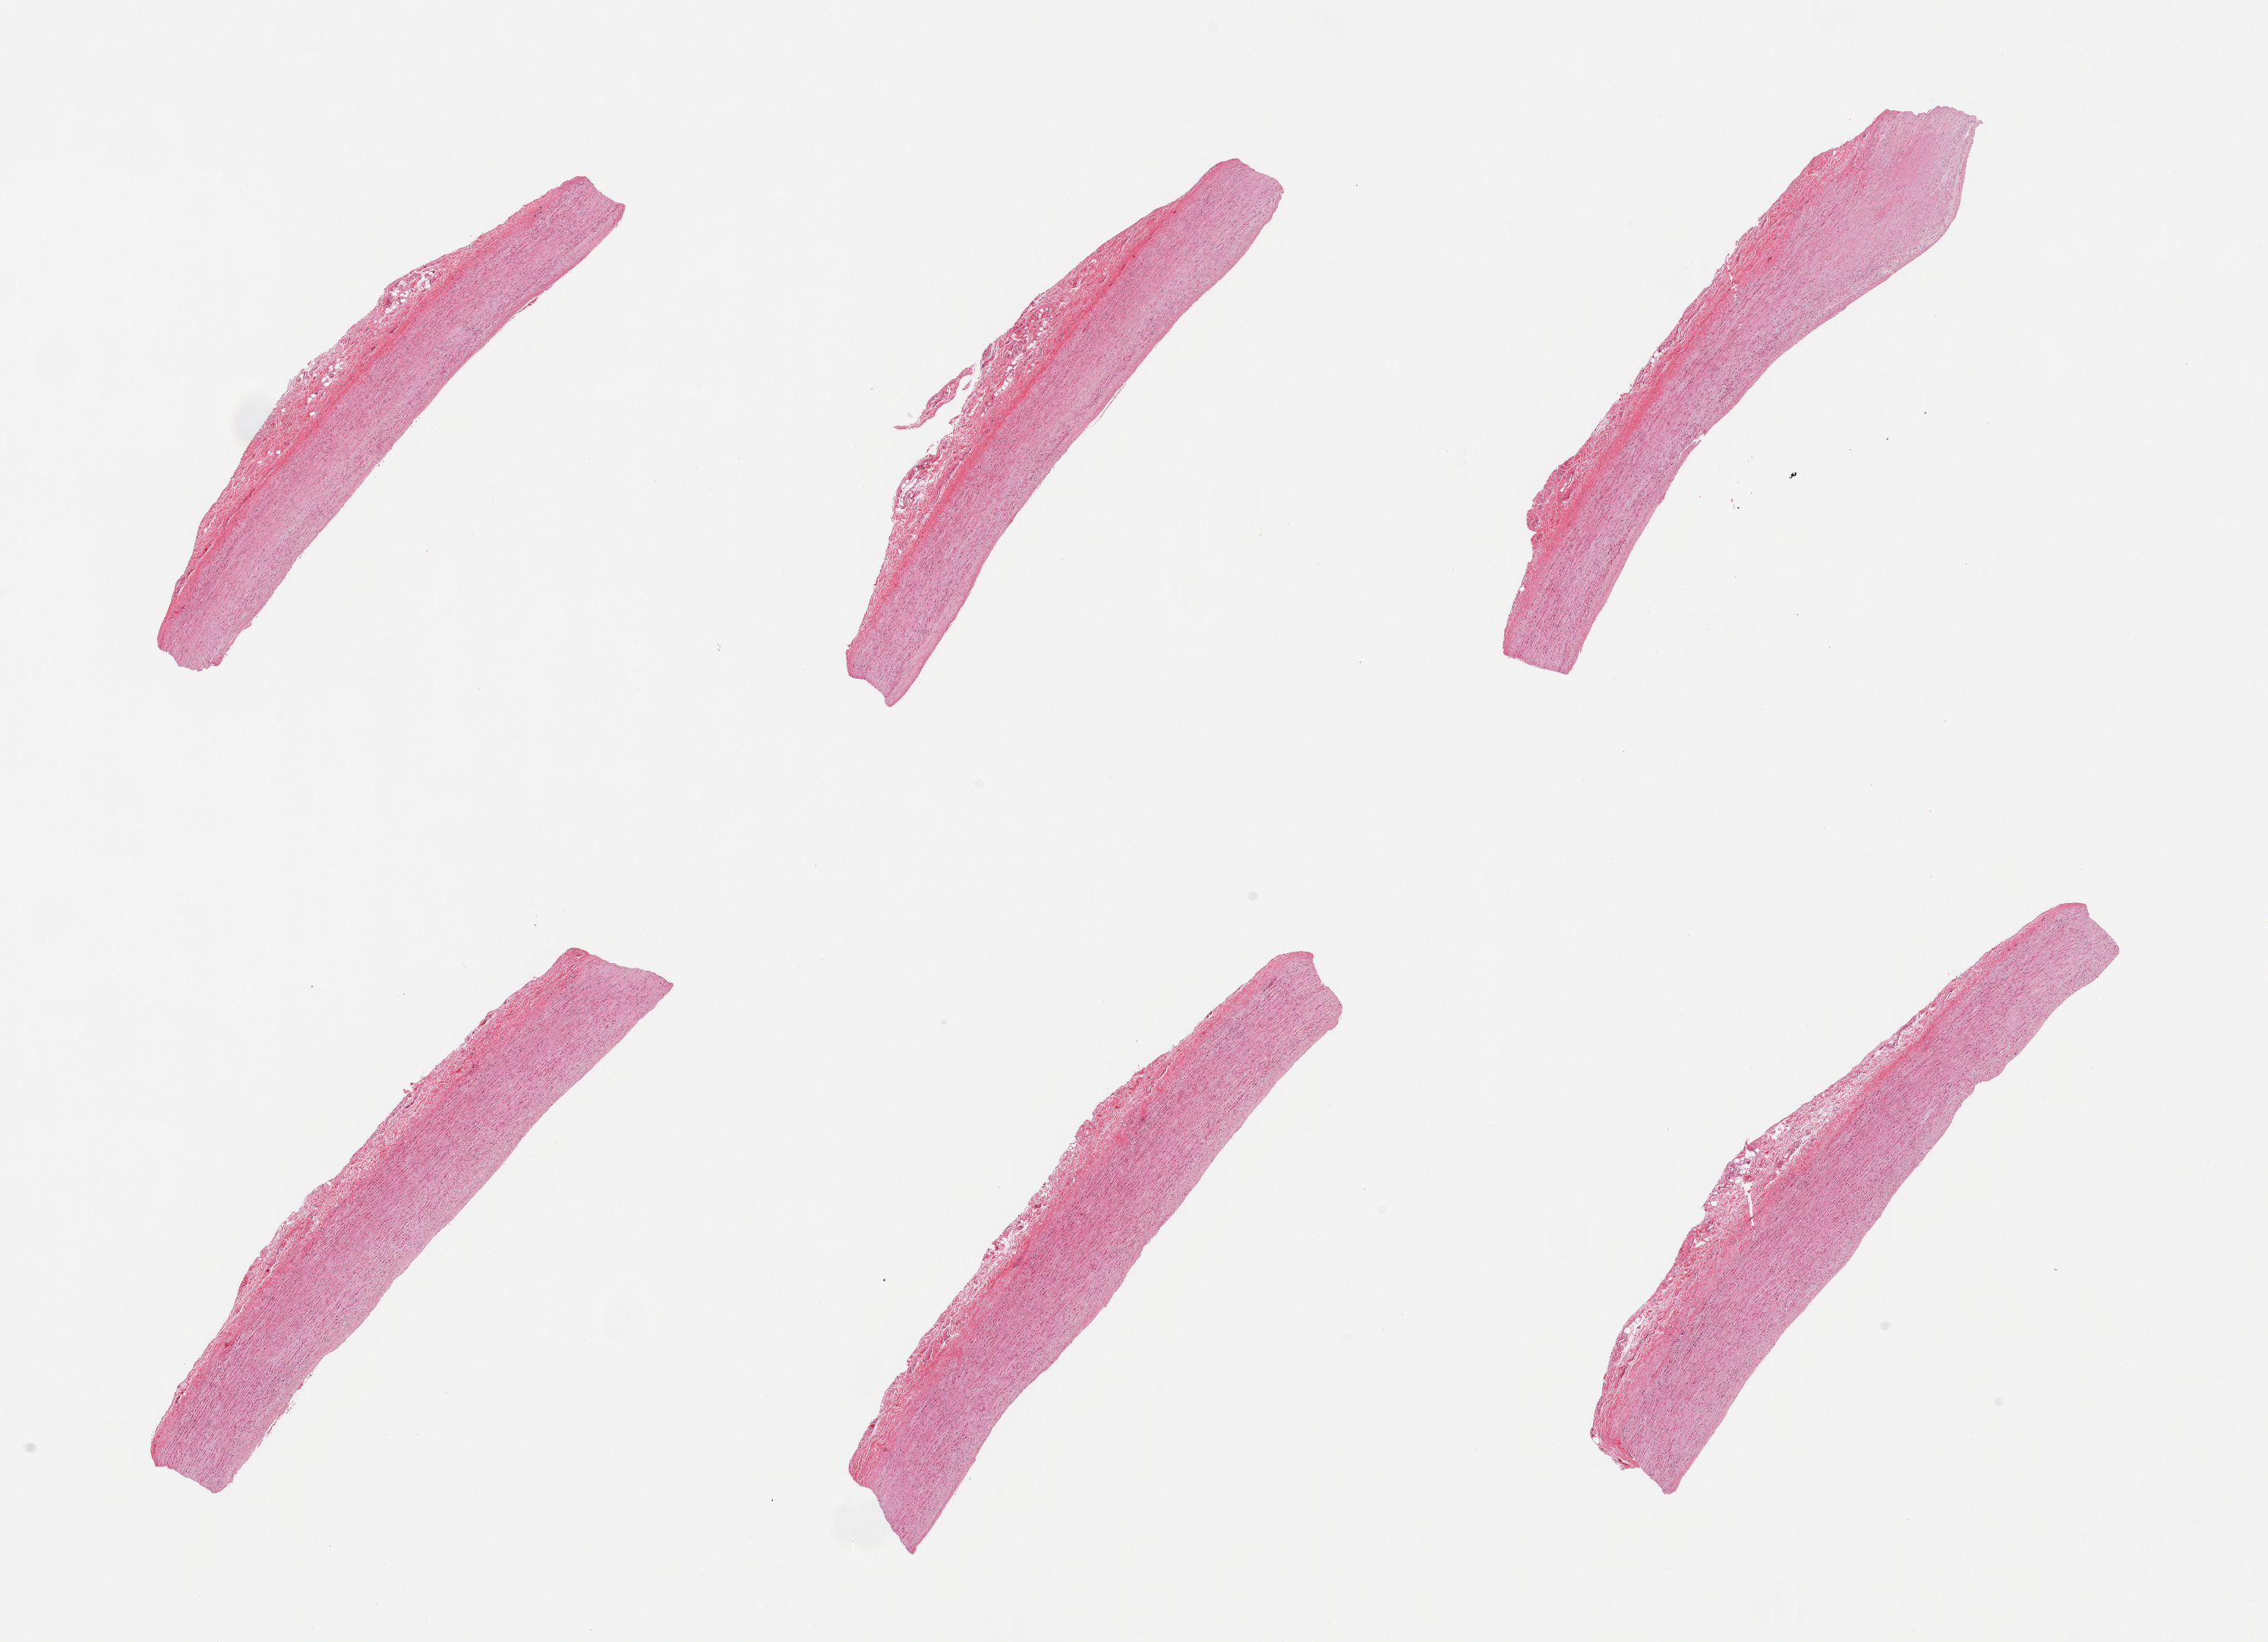
Digitized haematoxylin and eosin-stained section — shown as a low-resolution overview of the whole scanned area (about 23.6 x 17.1 mm, slide scanned at 20x); PAXgene-fixed paraffin-embedded (PFPE) section; target tissue: aorta; tissue donor sample. Donor sex: male.
Pathologist's review note for this sample: 6 pieces, atherosis up to ~0.5mm.